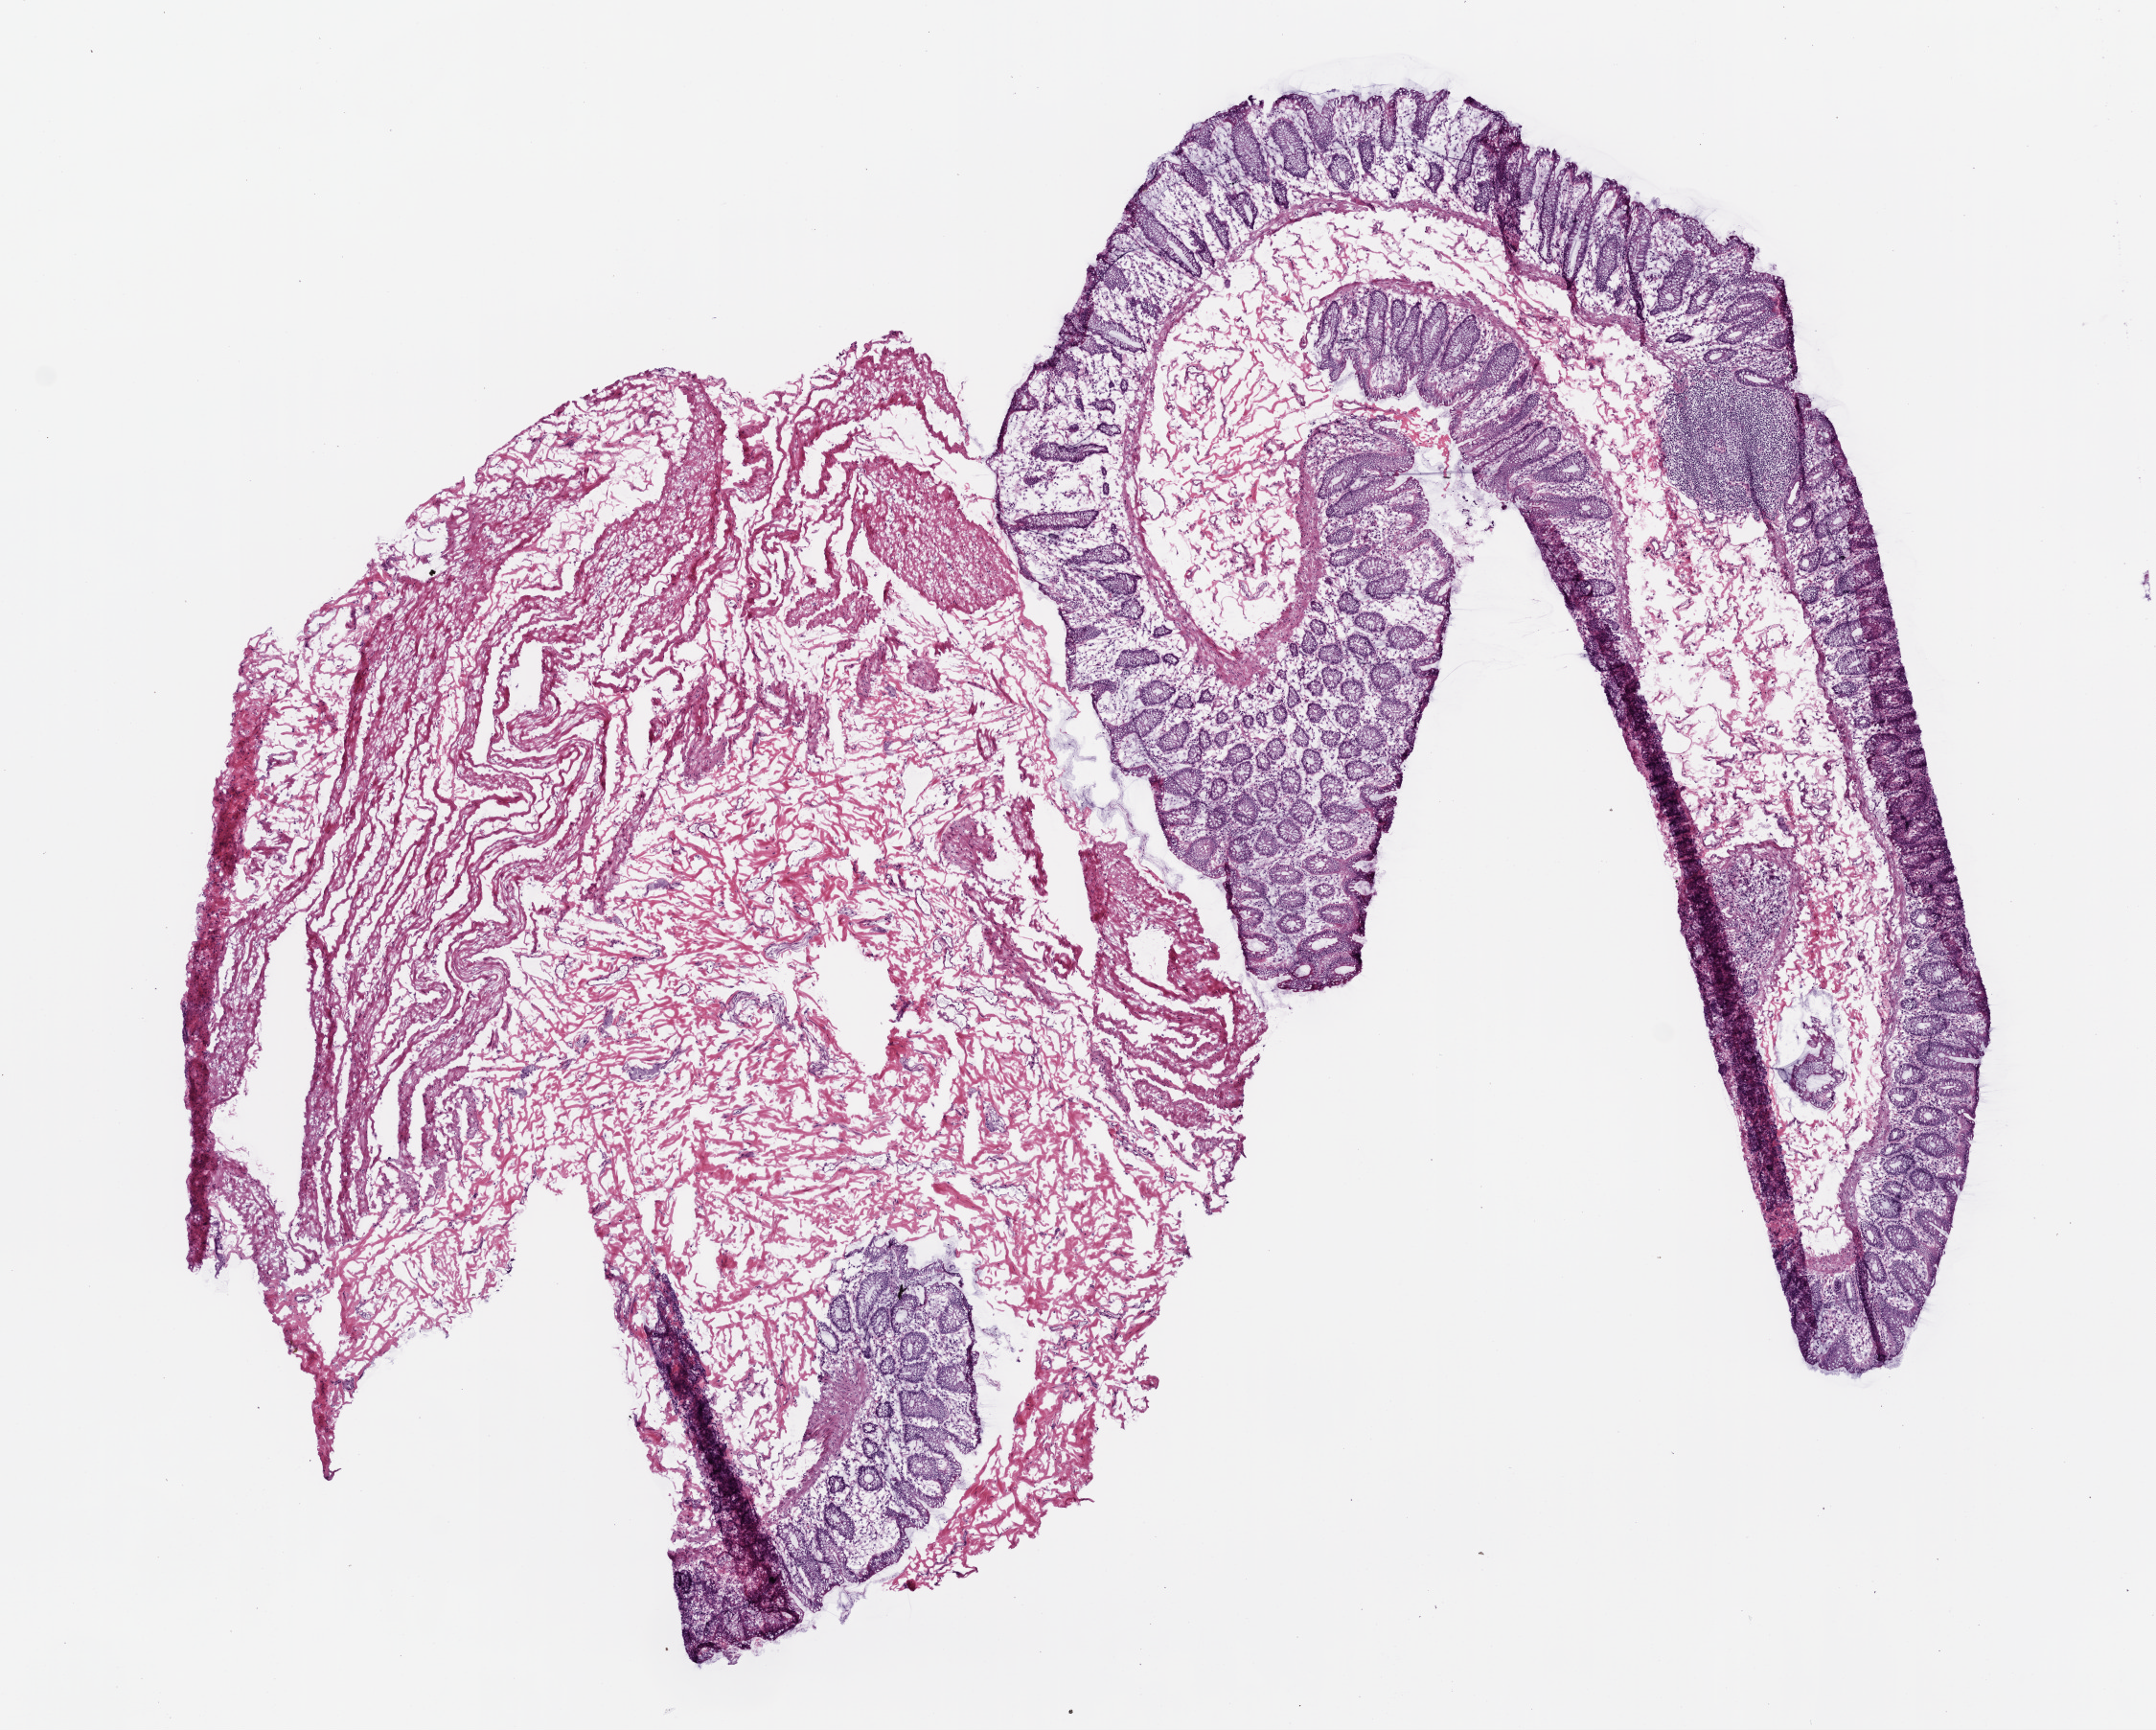
Digitized Hematoxylin and eosin (H&E) stained tissue section (whole slide), shown as a low-resolution overview of the whole scanned area (about 9.0 x 7.2 mm), frozen section from the top of the tissue portion, solid tissue normal (non-tumour tissue) sample from the colon. Patient sex: female.
This section: solid tissue normal (non-tumour) sample from the same patient. Patient diagnosis: Adenocarcinoma, NOS (ascending colon).